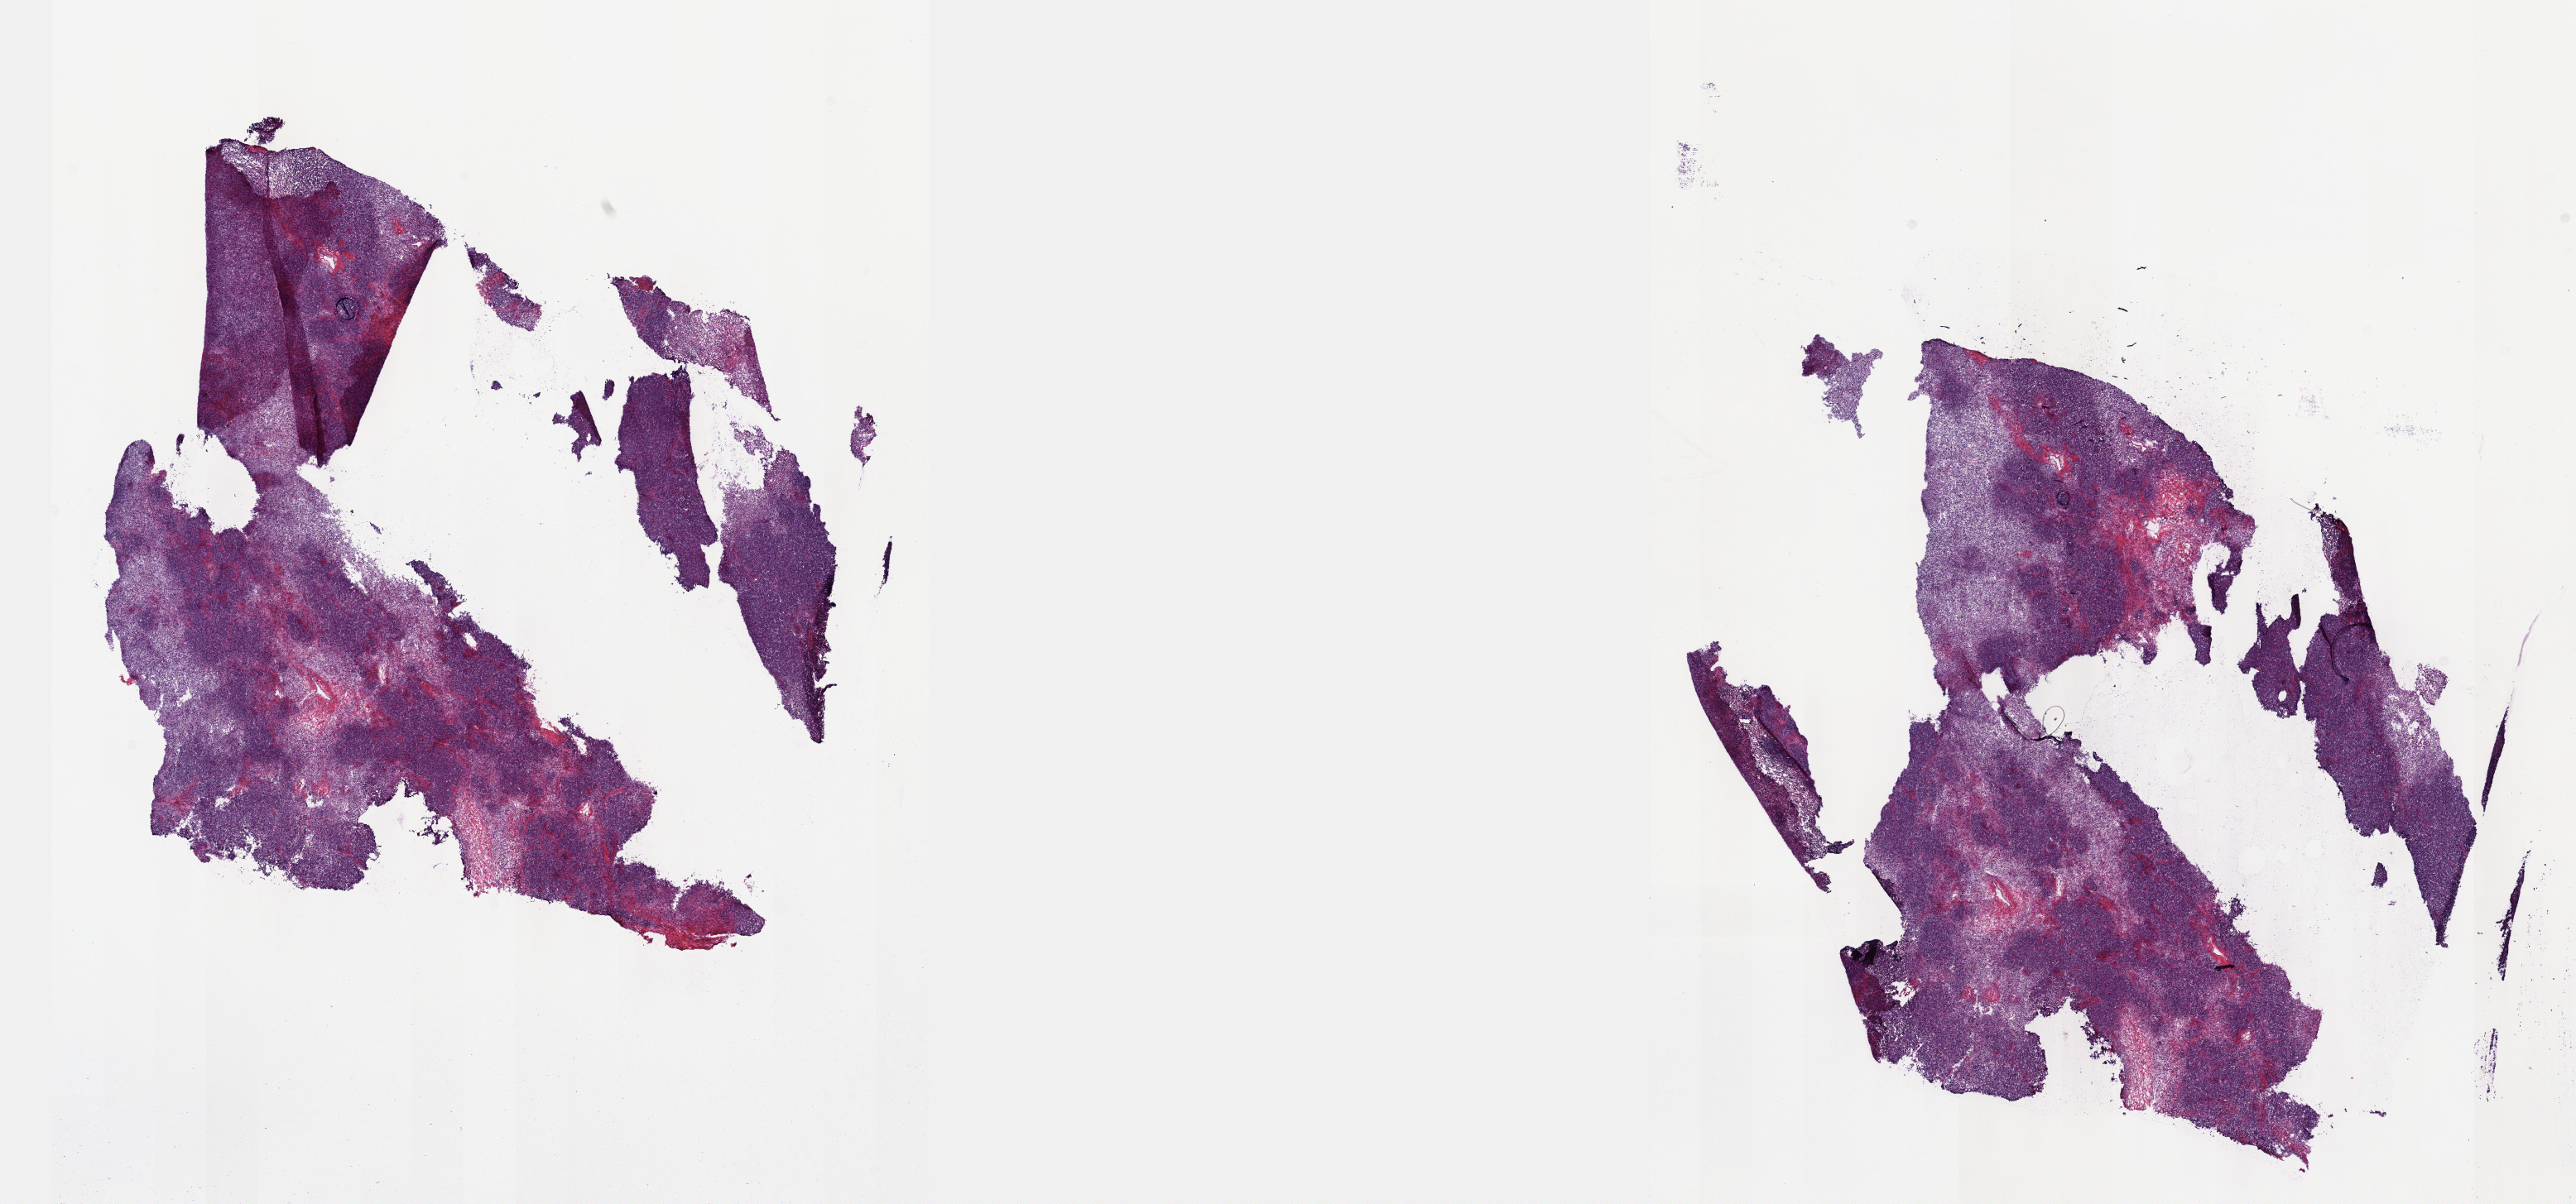
H&E-stained whole-slide image — low-resolution overview of the scanned area, about 25.1 x 11.8 mm (slide scanned at 40x); frozen section from the top of the tissue portion; sample: primary tumour, thymus. Female, age 77 years at initial diagnosis. Pathologist review of this section (percent, as recorded): tumour cells 100%, tumour nuclei 95%, normal cells 0%, stromal cells 0%, necrosis 0%. Inflammatory infiltration, as recorded: lymphocyte infiltration 0%, monocyte infiltration 0%, neutrophil infiltration 0%.
Histologic diagnosis: Thymoma, type AB, malignant.